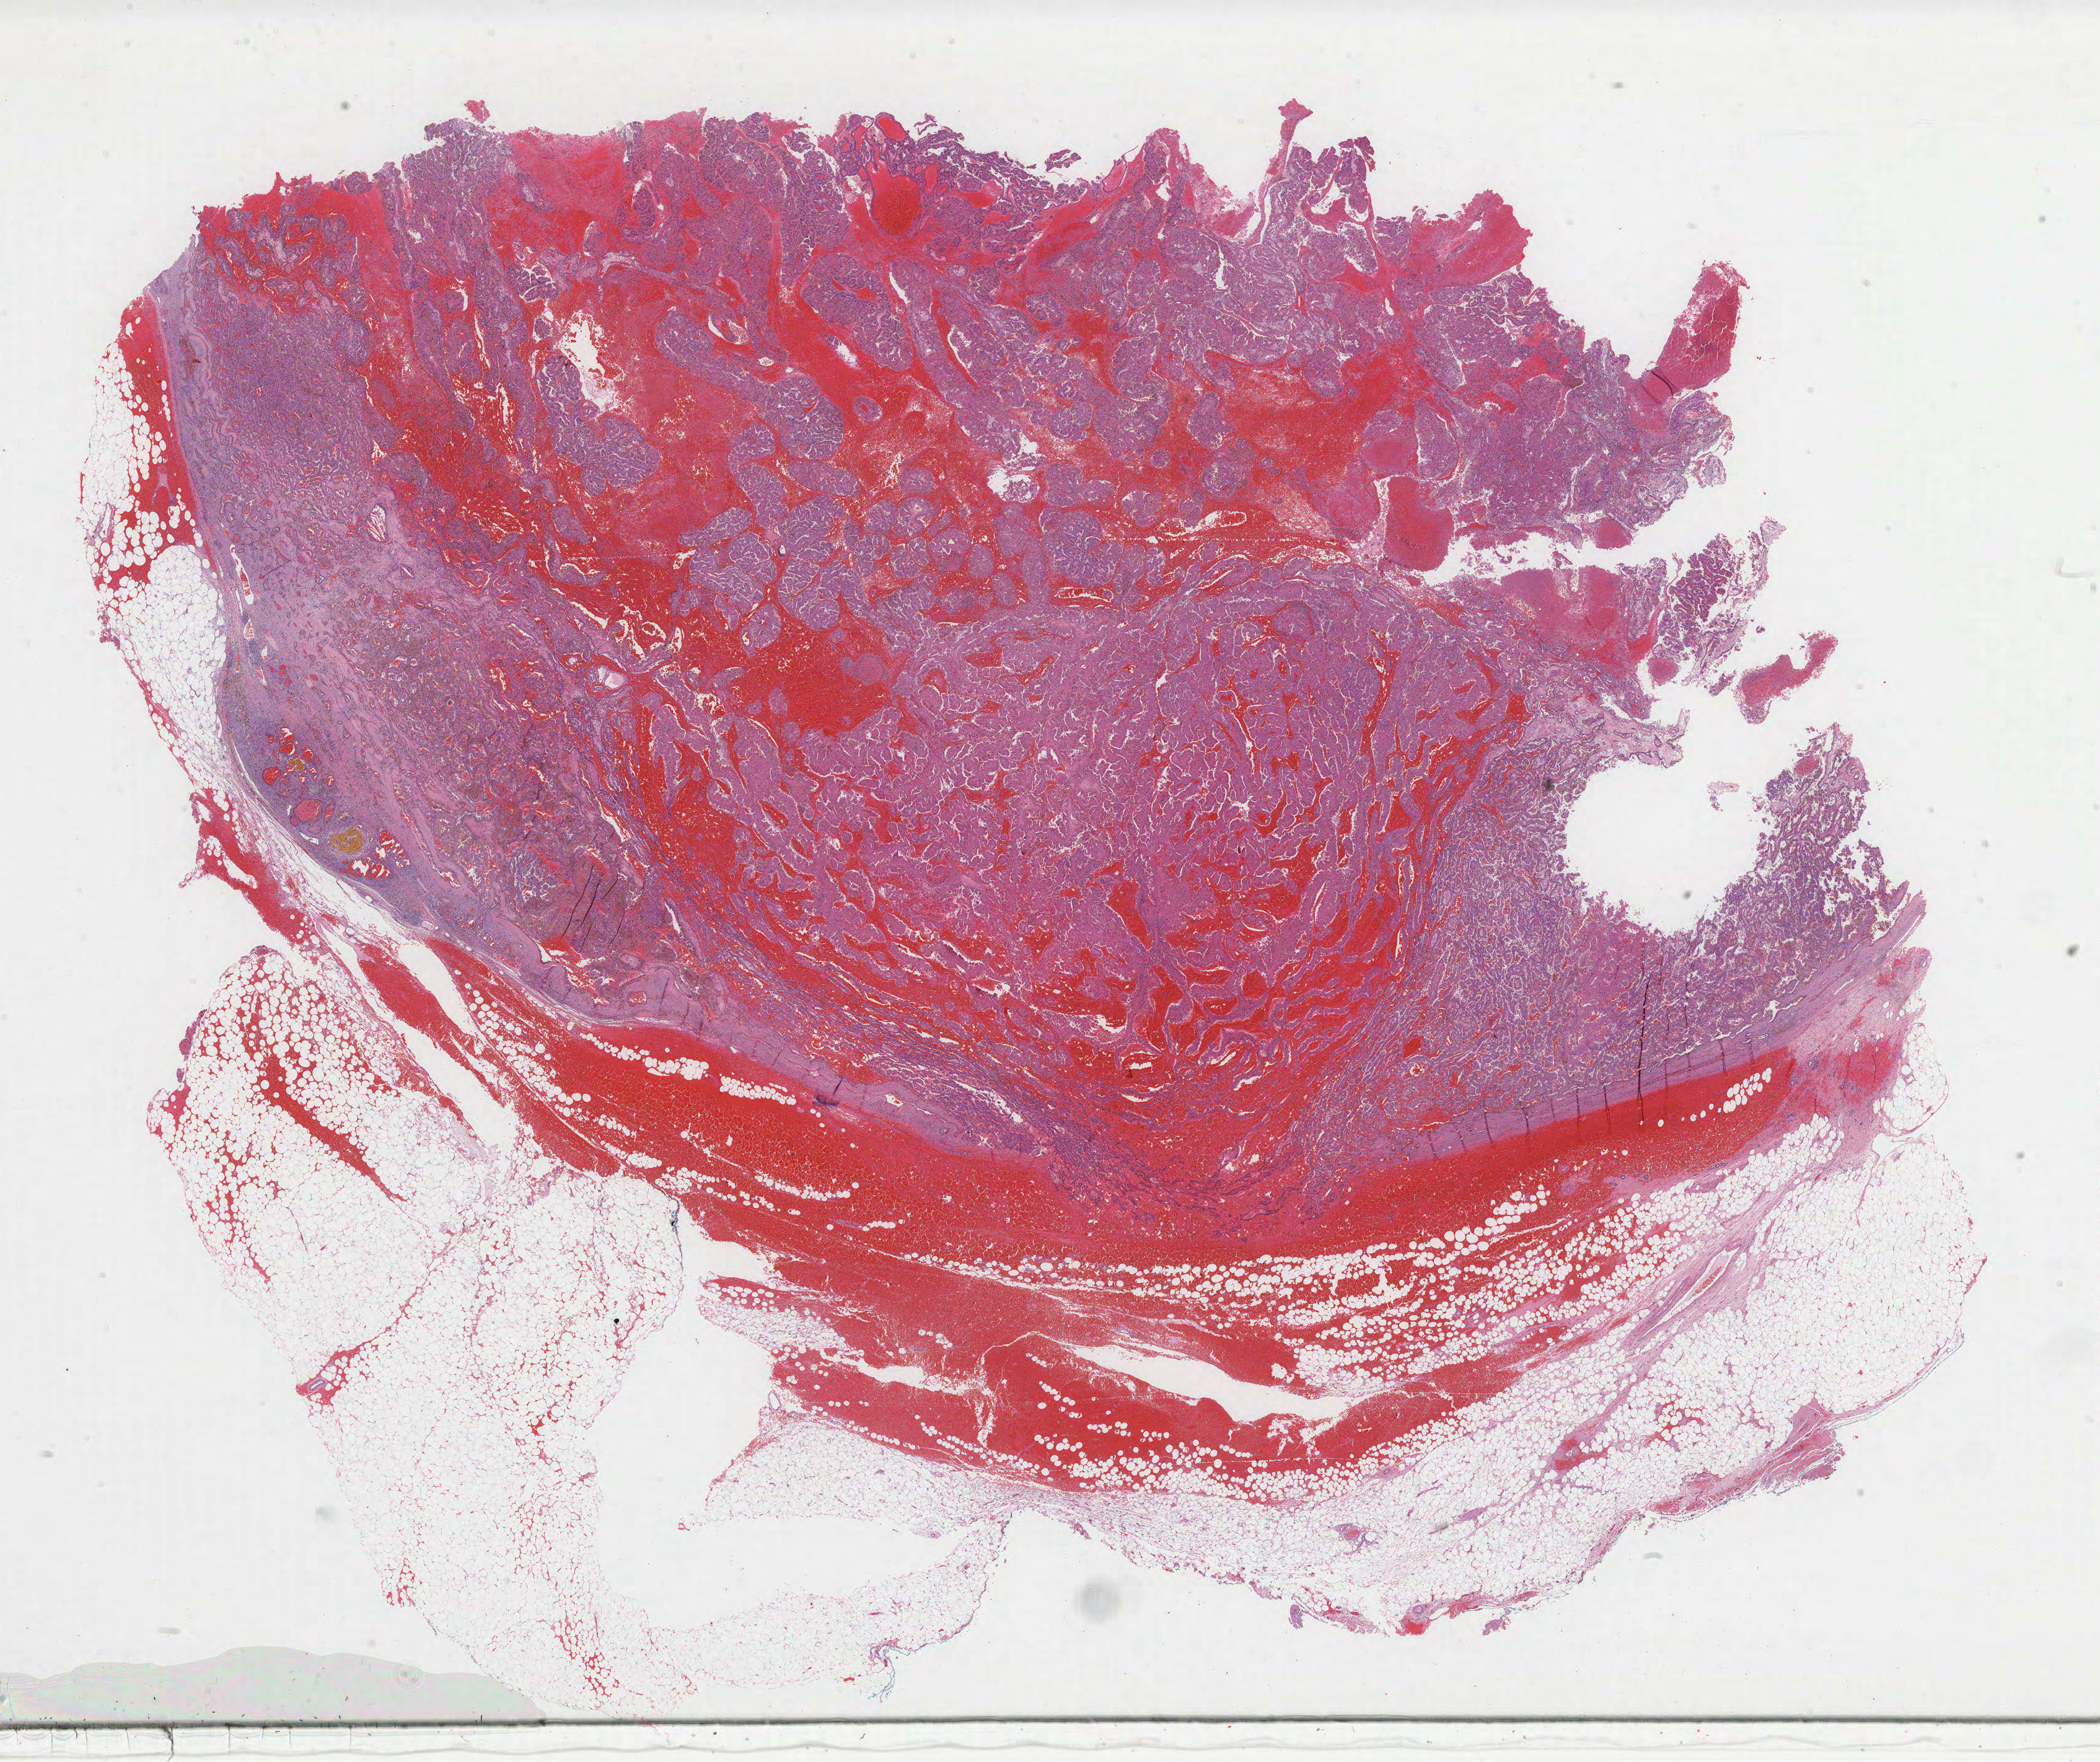
Hematoxylin and eosin (H&E) stained whole-slide image — low-resolution overview of the scanned area, about 27.4 x 23.0 mm, FFPE section, primary tumour sample from the kidney. Male, age 66 years at initial diagnosis.
Histologic diagnosis: Papillary adenocarcinoma, NOS.